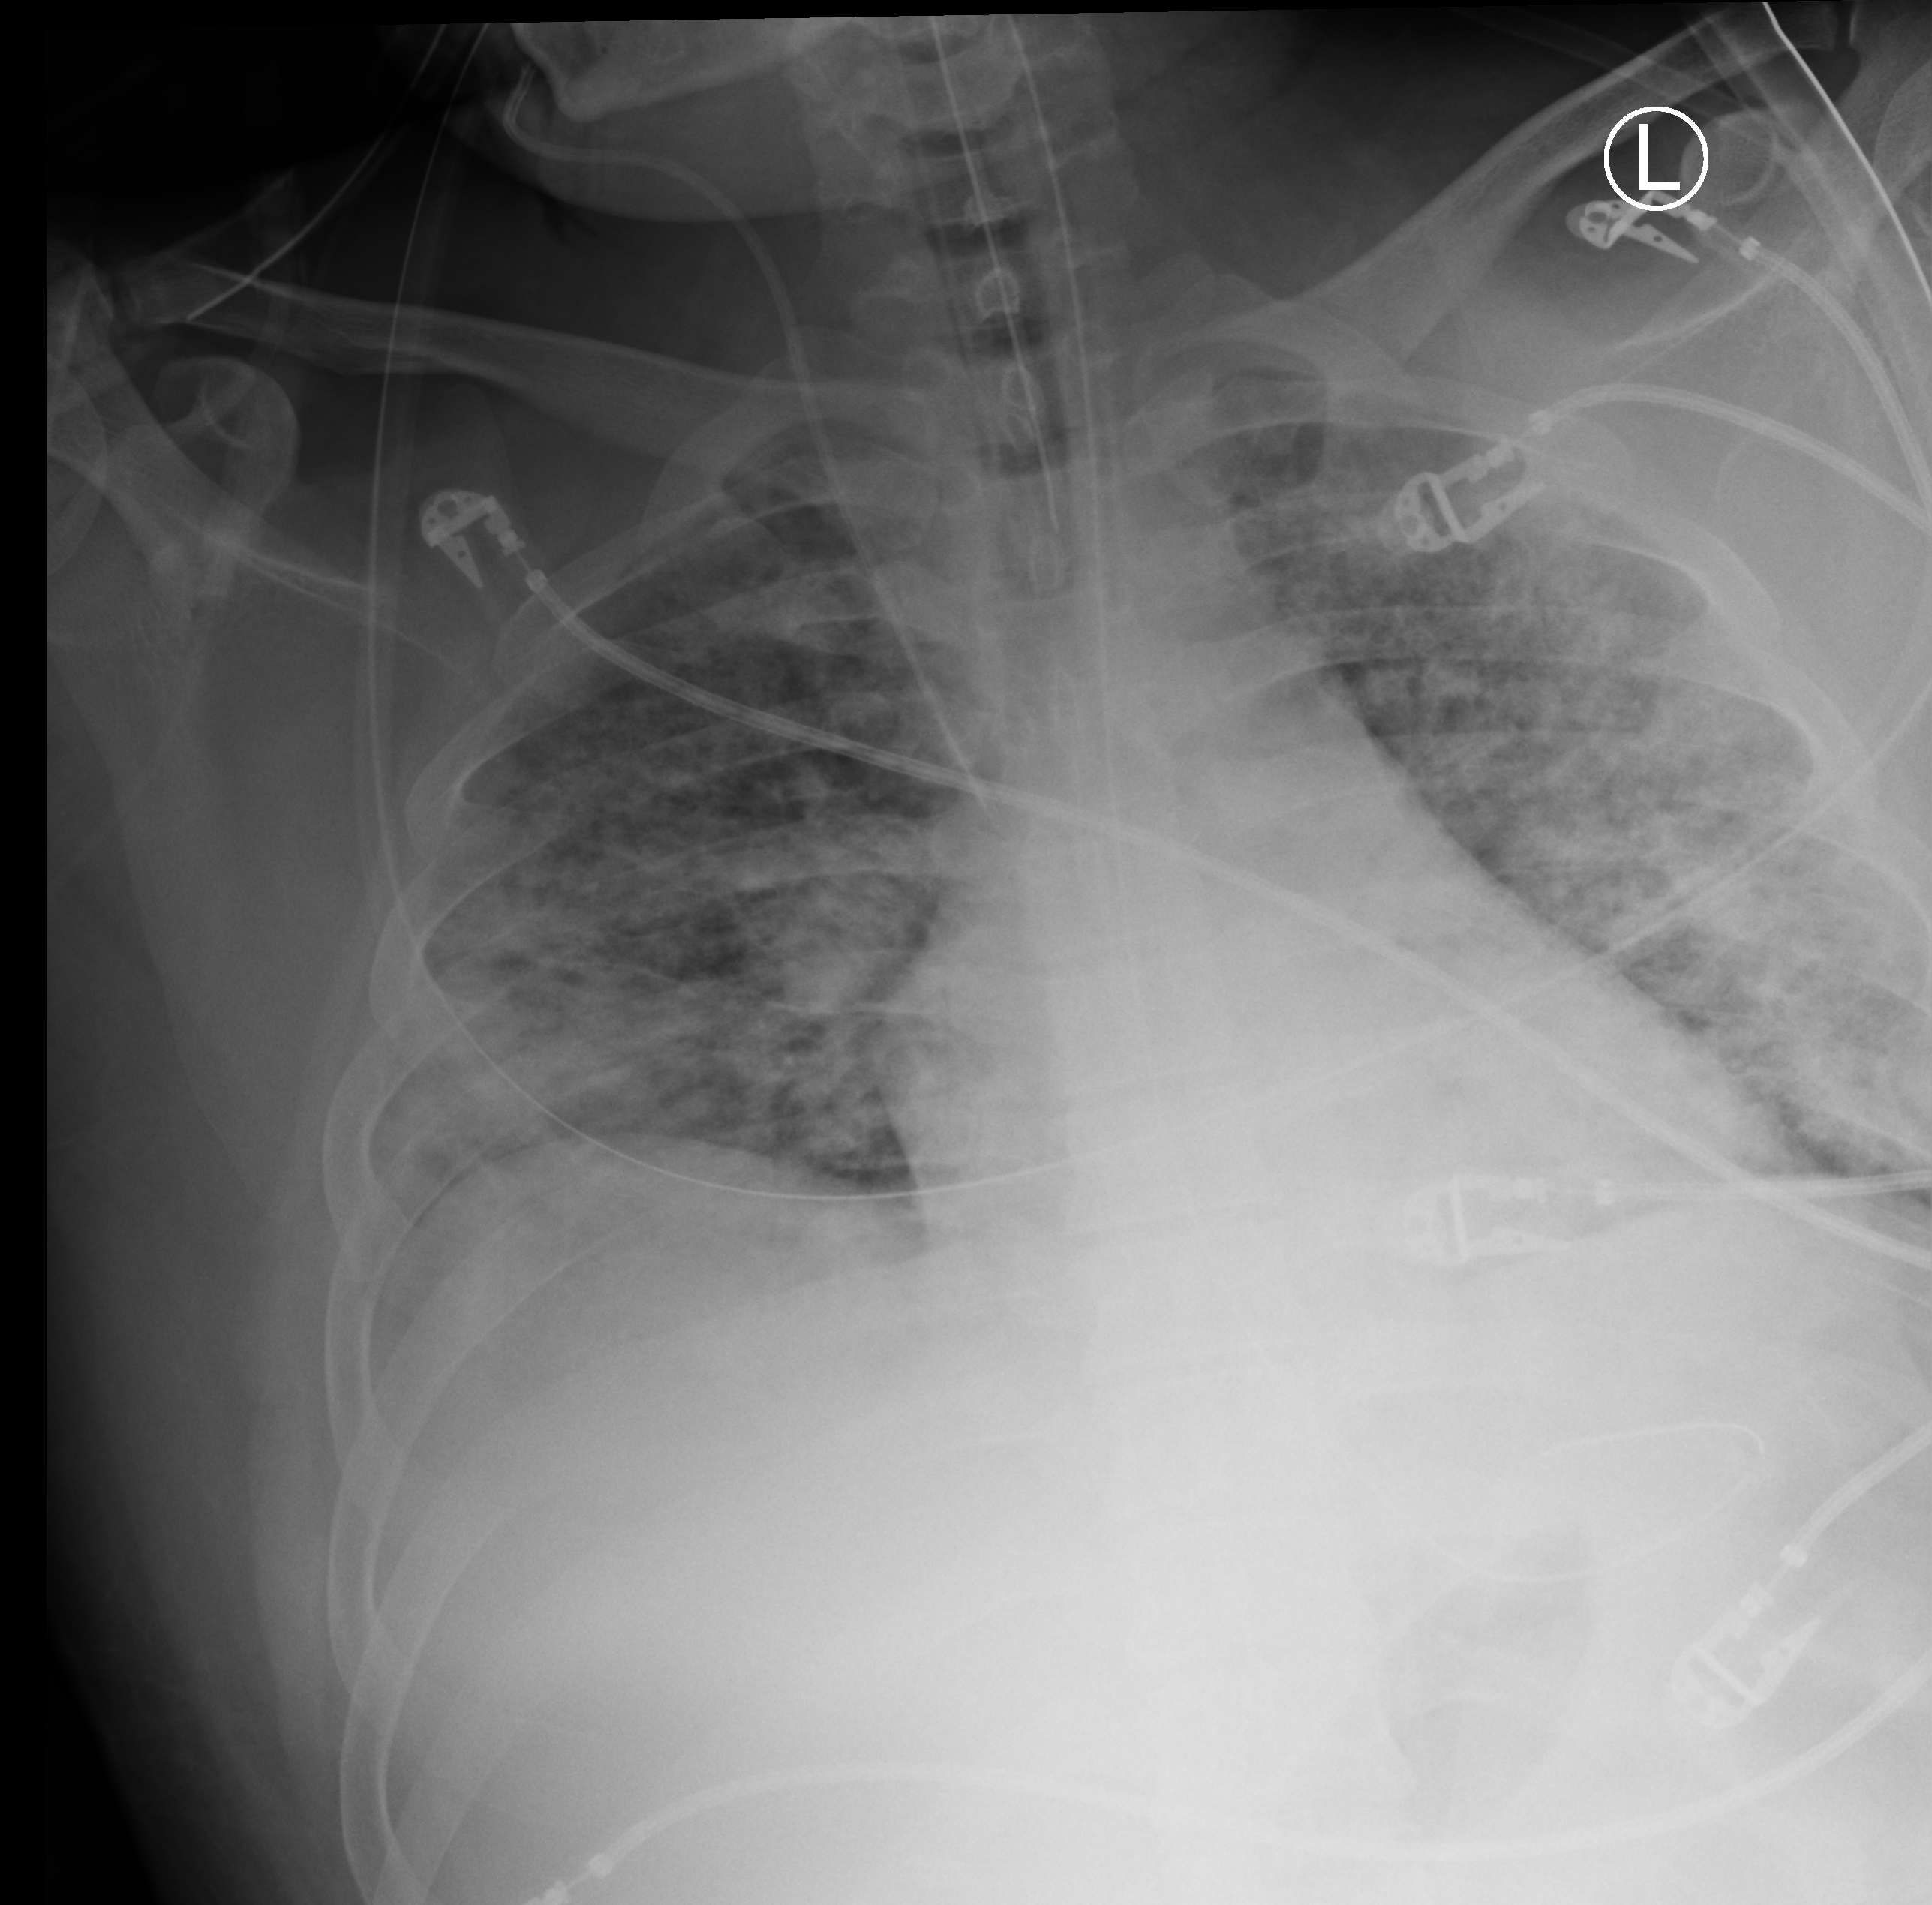
Bedside chest radiograph (computed radiography). Male patient hospitalised with COVID-19, age 18–59 years.
Admission-level facts for this patient (not findings on this image; timing relative to this image not recorded): admitted to intensive care during this hospital stay: yes; COPD (admission record): no.